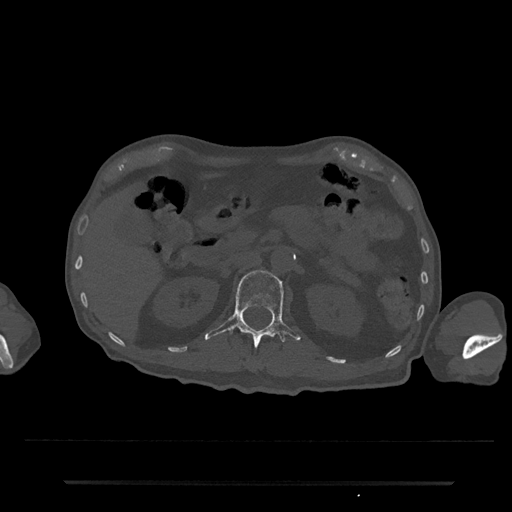
CT including the spine, one axial slice; slice 132 of 797 in the series (ordered by position); reconstruction kernel Br40s/3; 120 kVp; bone window (W 1800 / L 400 HU); 0.5 mm slice thickness; 512 × 512 image matrix, field of view 427 × 427 mm. Male patient, age 74 years. Case-level facts recorded for this patient, not image findings: primary cancer: prostate.
Structures marked on this image (semi-automatically segmented with operator editing):
- L1 vertebra: bounding box [x1, y1, x2, y2] px = [204, 270, 301, 347]